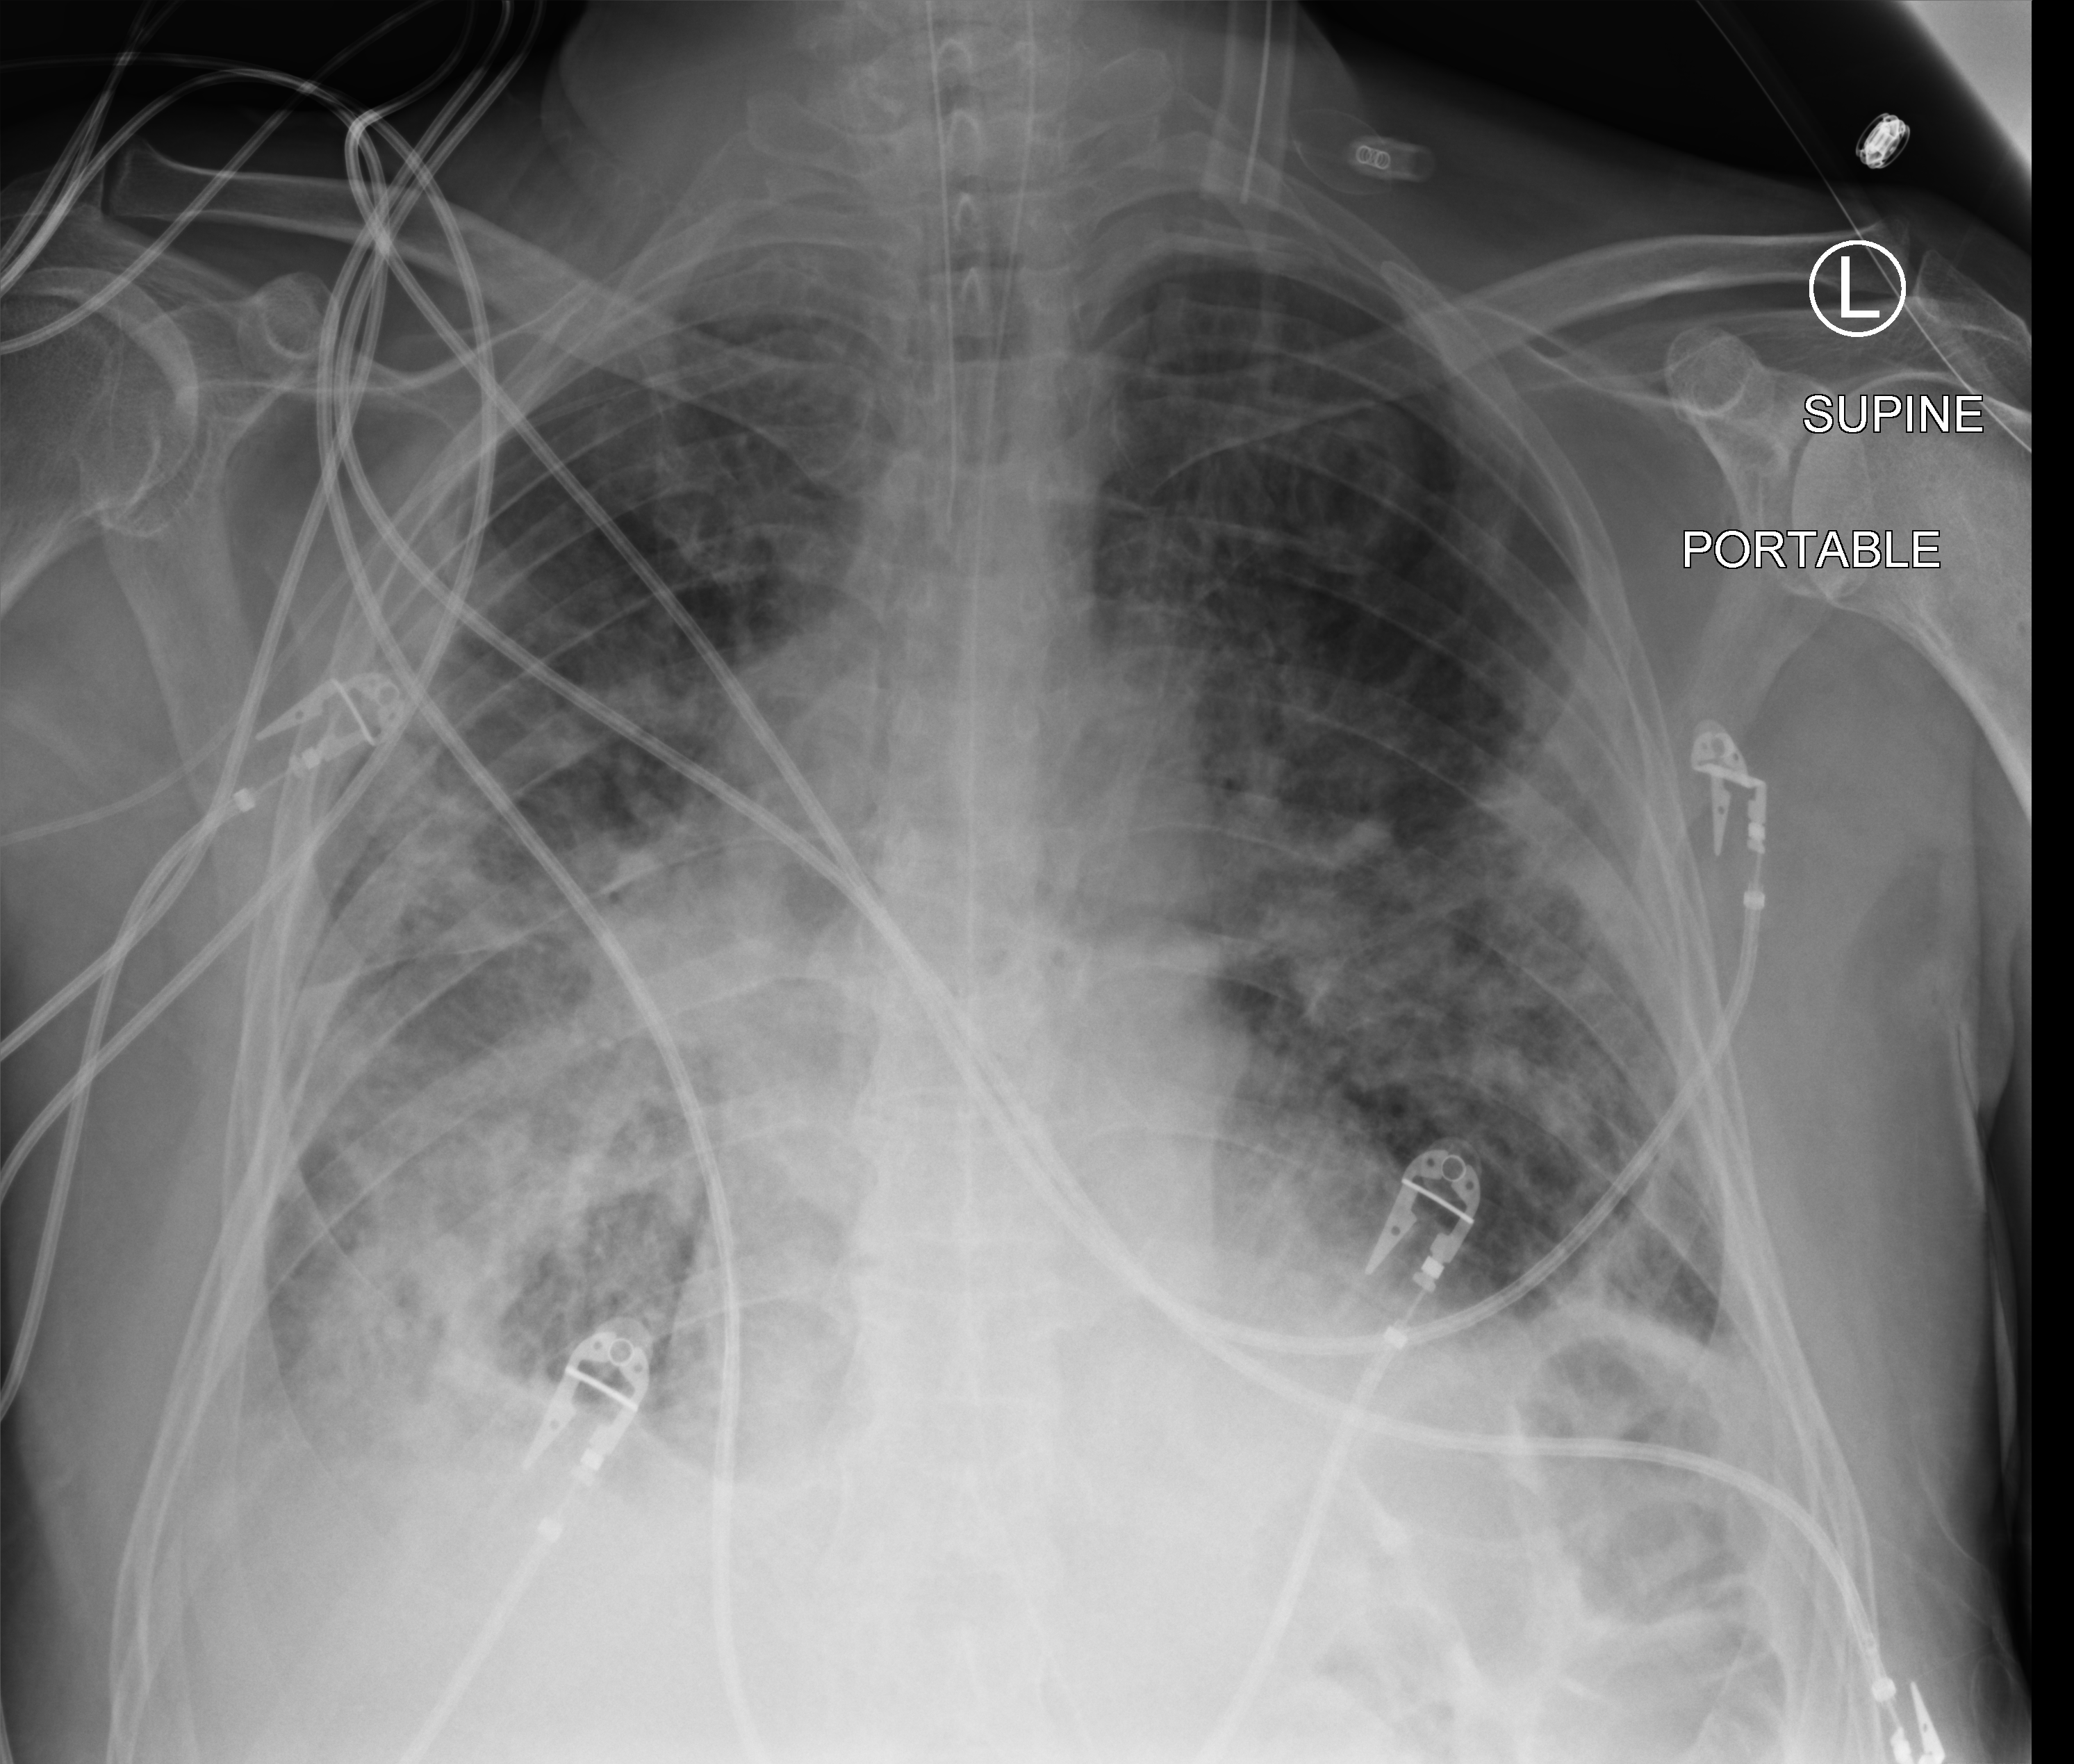
Portable chest radiograph, anteroposterior (AP) projection. Male patient hospitalised with COVID-19, age 75–90 years.
From the hospital-stay record, not from the radiograph (when in the stay this image was taken is not recorded): admitted to intensive care during this hospital stay: yes.